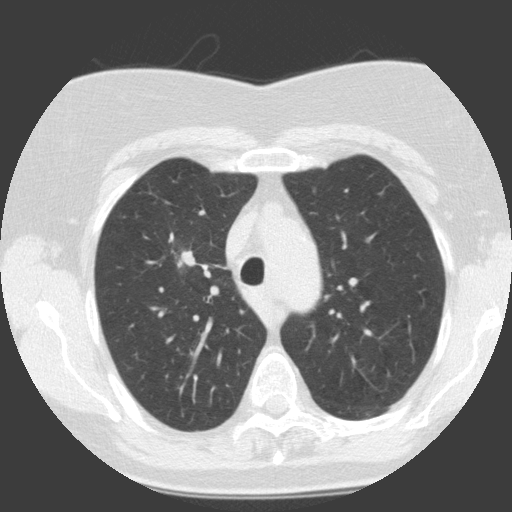
Low-dose screening chest CT, one axial slice; position 105 of 146 along the scan axis; 120 kVp; lung window (W 1500 / L -600 HU); 2 mm slice thickness; 512 × 512 image matrix.
Structures marked on this image (outlined manually by an expert reader):
- lesion 1 (tumor, upper lobe of right lung): bounding box <177,250,195,268> (left, top, right, bottom; pixels)